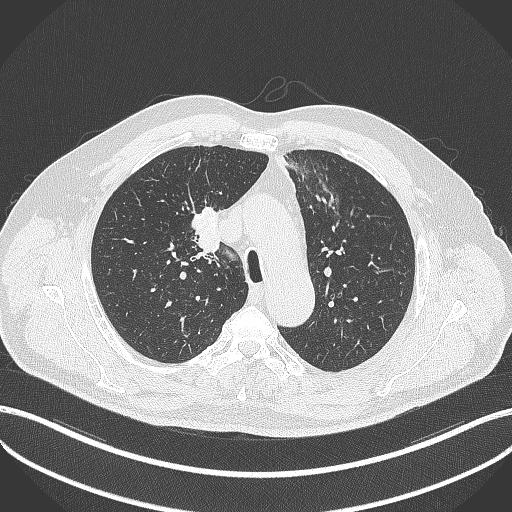
Chest CT, one axial slice. Position 282 of 411 along the scan axis. Reconstruction kernel B70f. 120 kVp. Lung window (W 1500 / L -600 HU). 1 mm slice thickness. 512 × 512 image matrix, field of view 400 × 400 mm. Patient: male, 60 years. Case-level facts recorded for this patient, not image findings: clinical TNM (as recorded): T1b N1 M0.
Outlined on this slice (bounding box drawn by a radiologist):
- lung tumour (recorded histology: squamous cell carcinoma): bounding box [x1, y1, x2, y2] px = [189, 202, 223, 257]